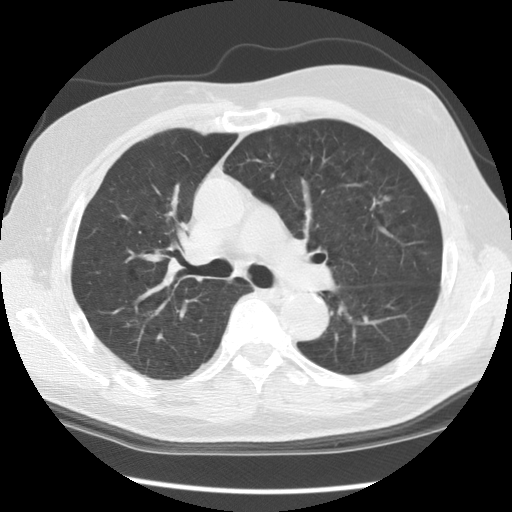
Low-dose screening chest CT, axial slice. Second annual screen. Lung window (W 1500 / L -600 HU). 2.5 mm slice thickness. Male, age 70 years at enrolment. Current smoker at enrolment.
- Expert reader's lesion annotation, bounding box [x1, y1, x2, y2] px = [342, 181, 402, 236].
- The screening reader recorded 3 non-calcified nodules or masses ≥4 mm on this exam; which of them this box marks is not recorded.
- Official screen result: positive, other.
- Lung cancer was diagnosed 396 days after this screen (after the third annual screen): adenocarcinoma, NOS, left upper lobe, moderately differentiated (G2), stage IIIA (AJCC 6th edition), 17 mm at pathology.